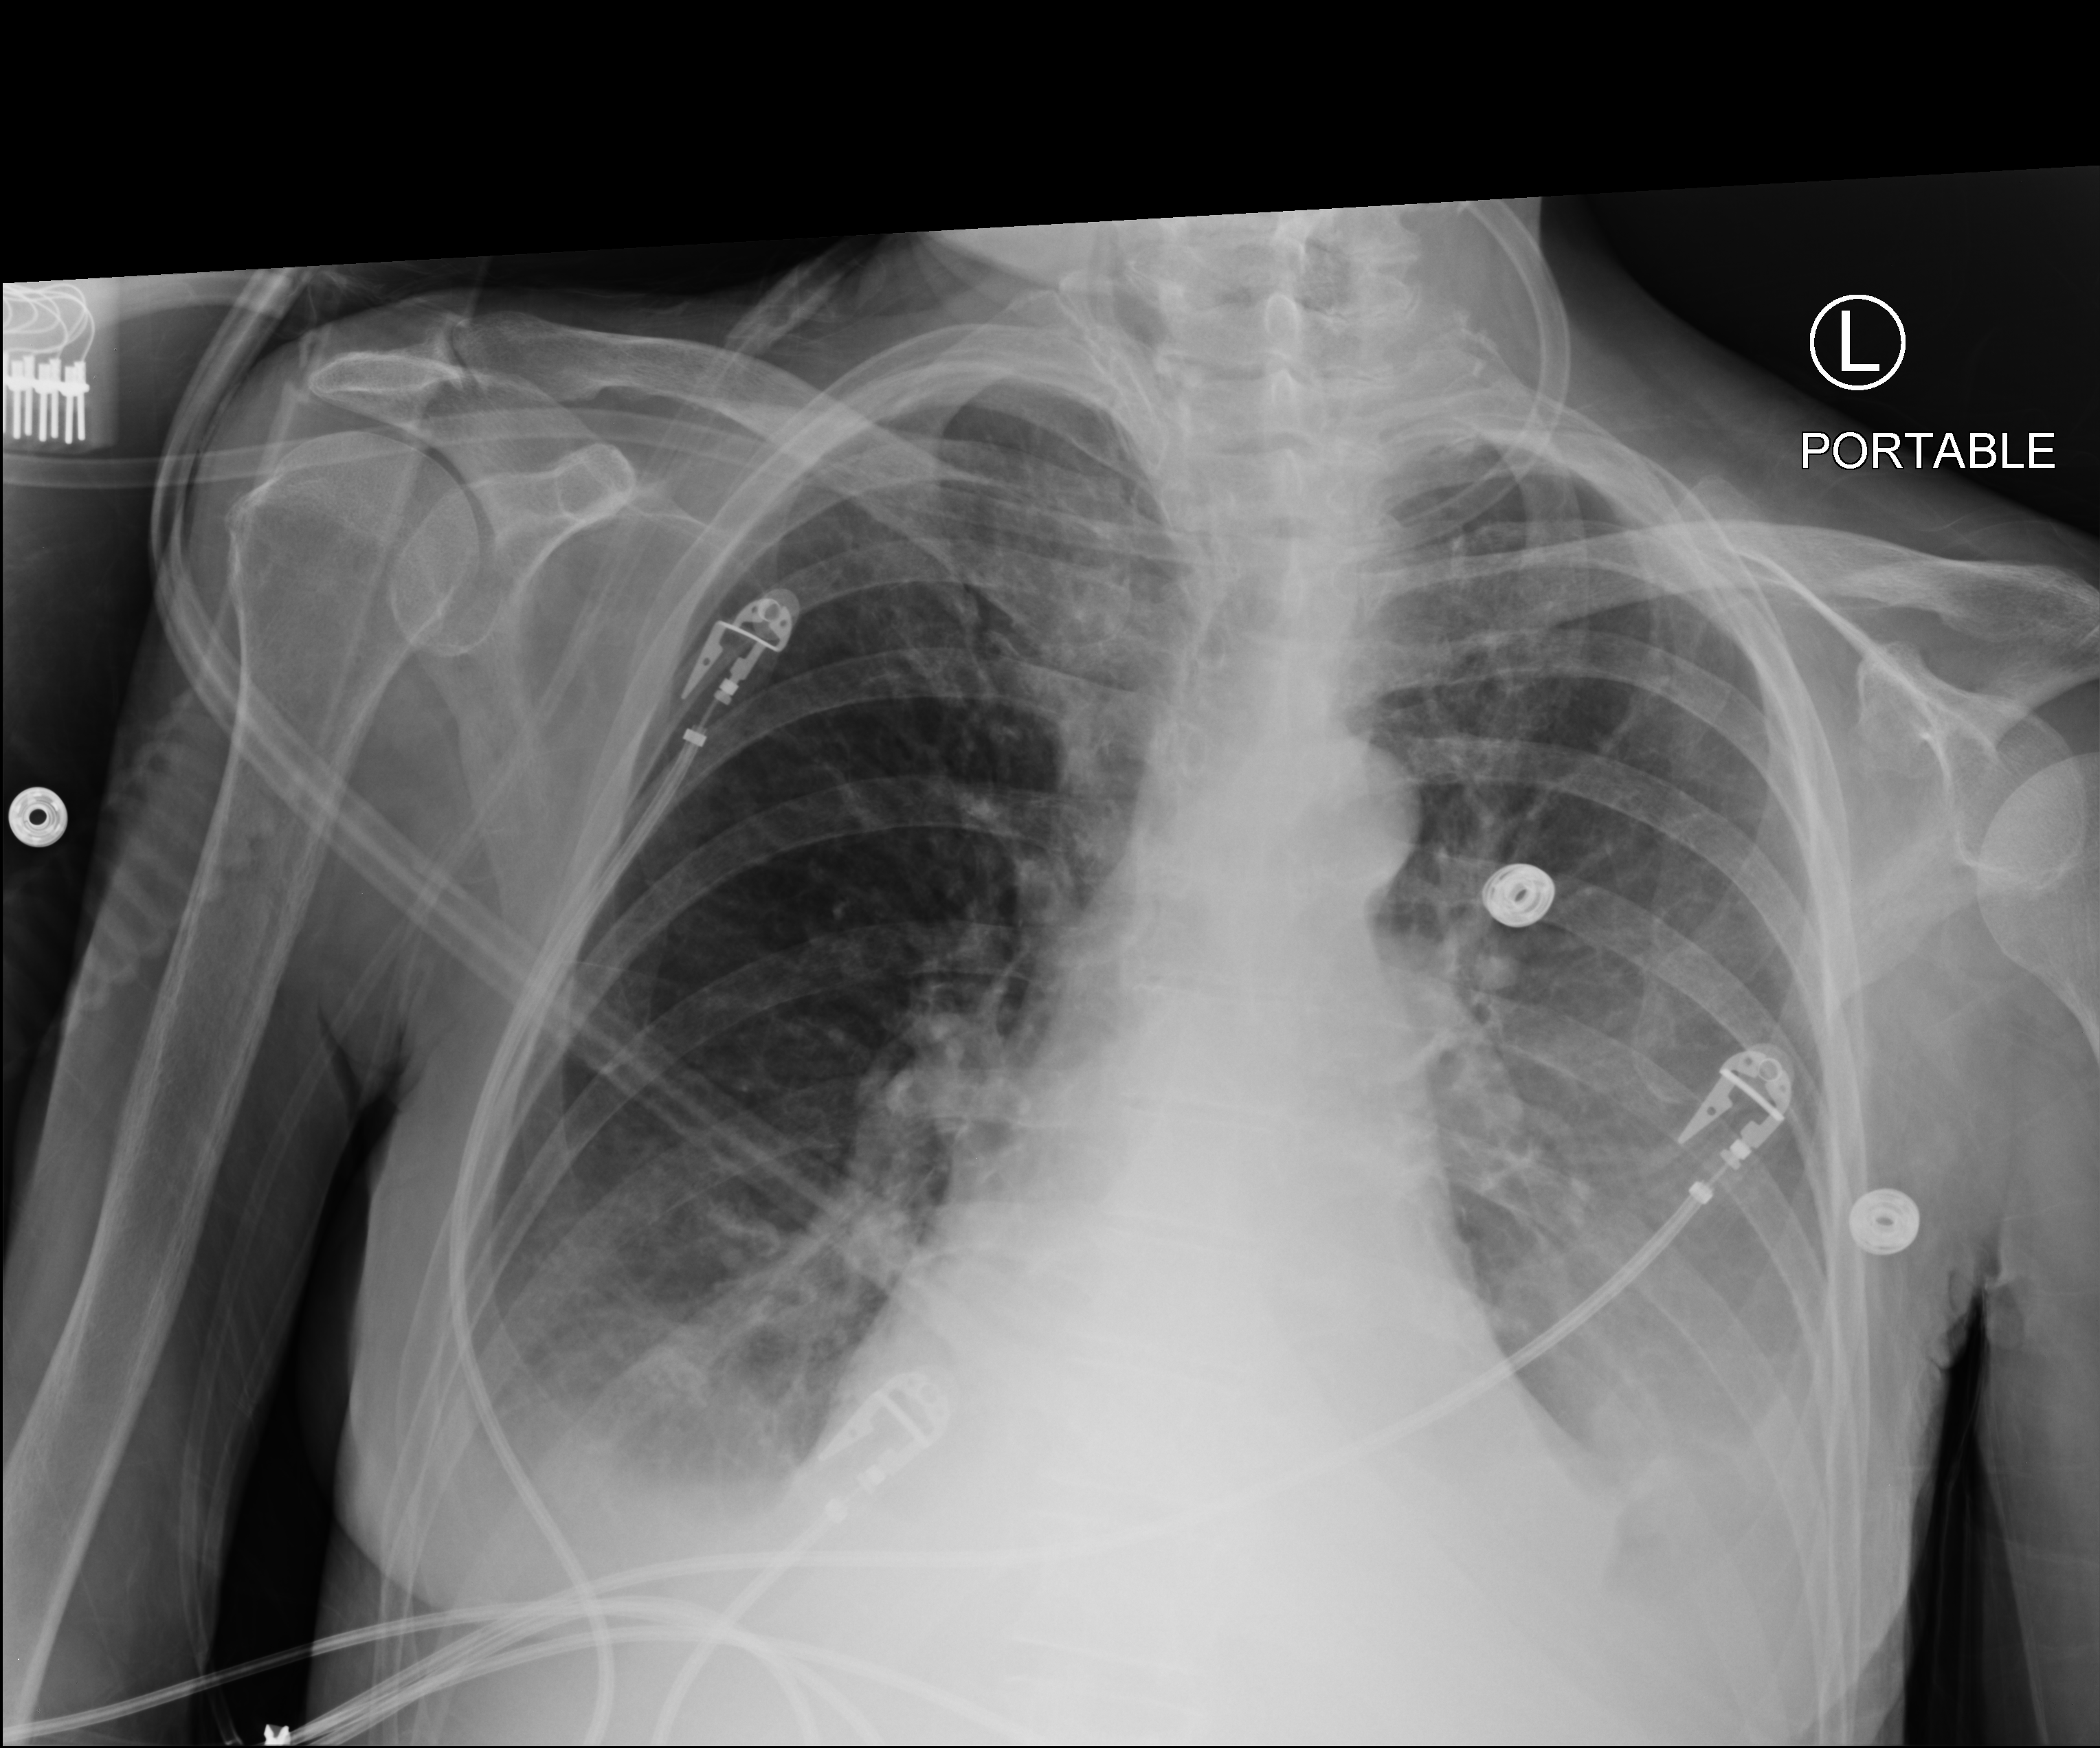
Portable chest radiograph, anteroposterior (AP) projection. Patient hospitalised with COVID-19; female, aged 60–74 years.
Hospital-stay facts (about this admission, not read from this image; timing relative to this image not recorded):
- mechanically ventilated during this hospital stay: yes
- admitted to intensive care during this hospital stay: yes